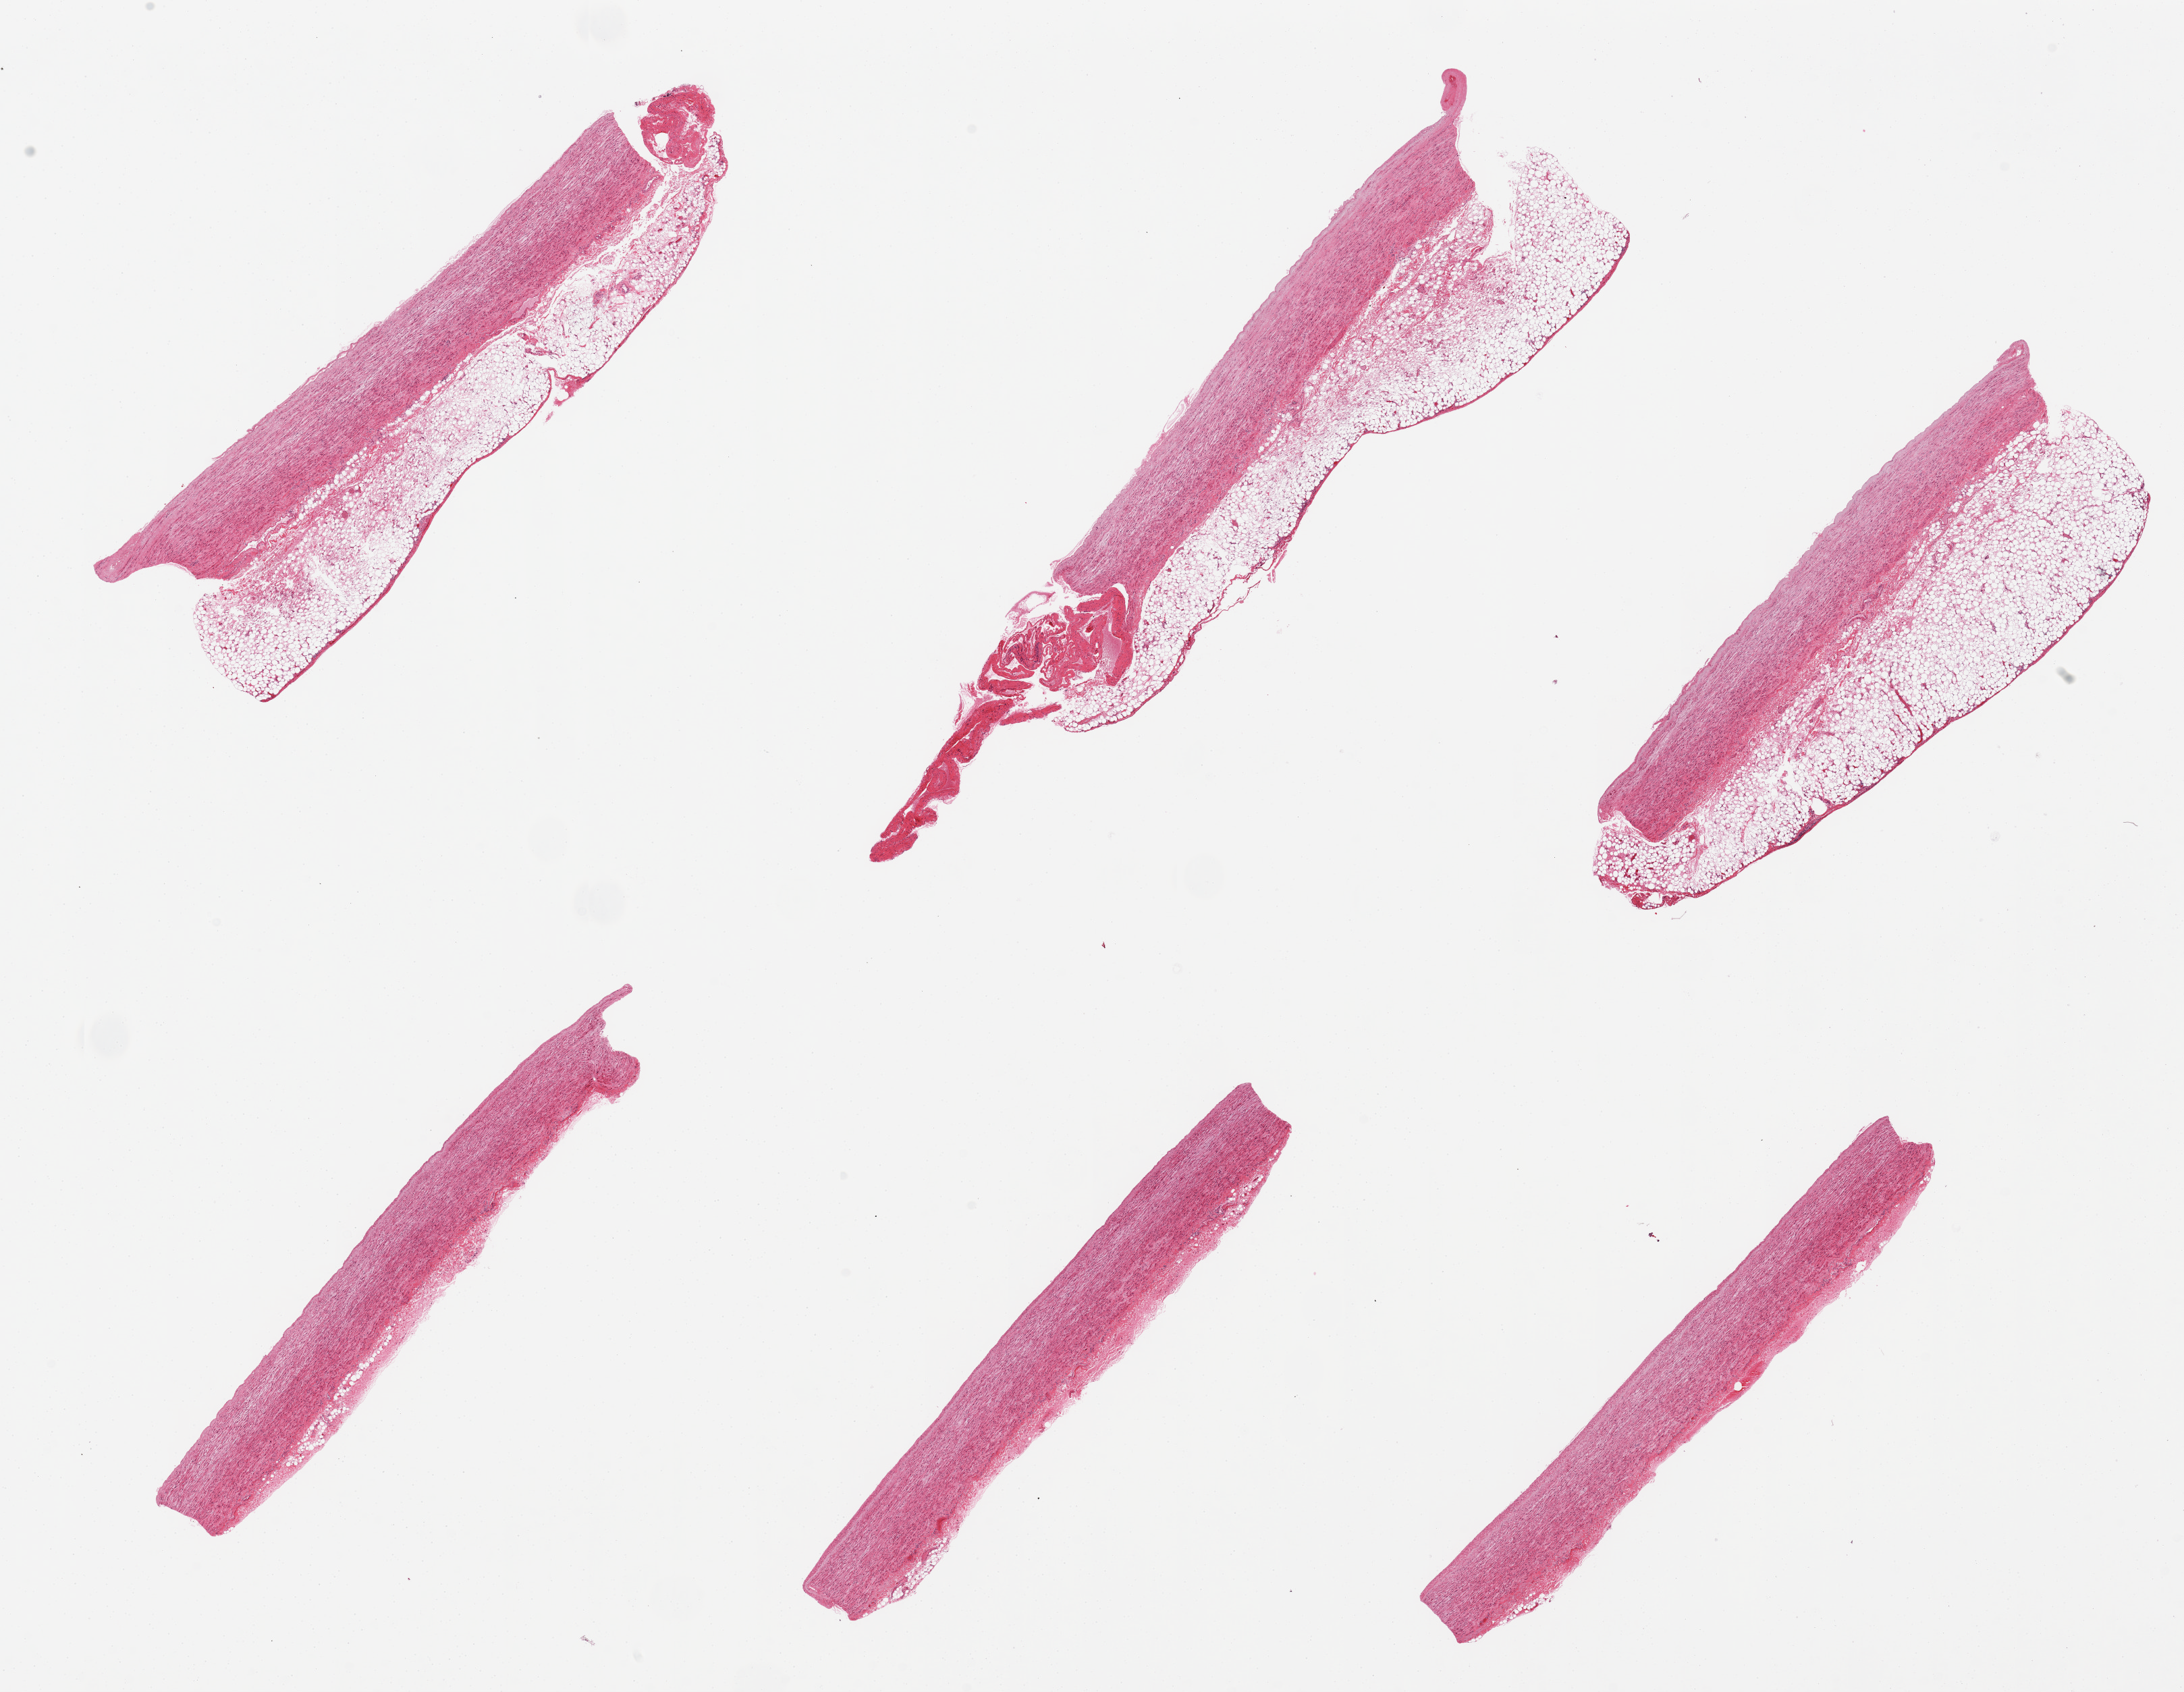
Digitized hematoxylin and eosin (H&E)-stained section, low-resolution overview of the scanned area, about 25.6 x 19.8 mm (slide scanned at 20x); PAXgene-fixed, paraffin-embedded tissue; sampled site (target tissue): aorta; tissue donor sample.
• pathologist's review note for this sample: 6 pieces, adherent serosal fat up to ~2mm thick